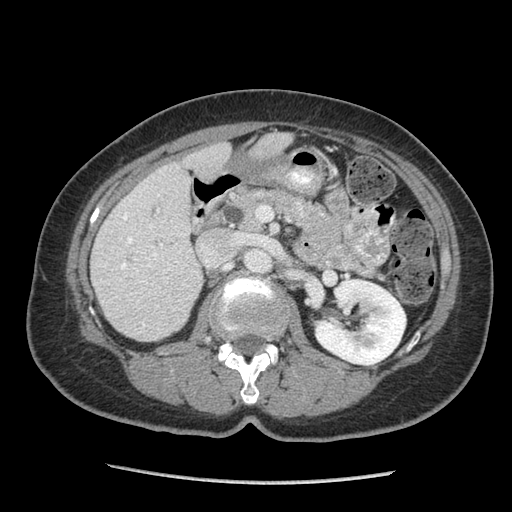
Contrast-enhanced abdominal CT (liver protocol), one axial slice. Slice 35 of 105 in the series (ordered by position). 140 kVp. Soft-tissue window (W 400 / L 40 HU). 2.5 mm slice thickness. 512 × 512 image matrix. Case-level facts recorded for this patient, not image findings: diagnosis: hepatocellular carcinoma (patient treated with transarterial chemoembolisation; whether this scan precedes or follows treatment is not stated here); TNM stage (as recorded): Stage-I; Child-Pugh class: A; tumour nodularity: uninodular; tumour size: 11.1 cm.
Outlined on this slice (semi-automatically segmented with operator editing):
- liver parenchyma outside the tumour (the mass and vessels are separate outlines, so this box may not span the whole liver): bounding box <90,132,292,340> (left, top, right, bottom; pixels)
- liver vessels: <121,194,191,327>